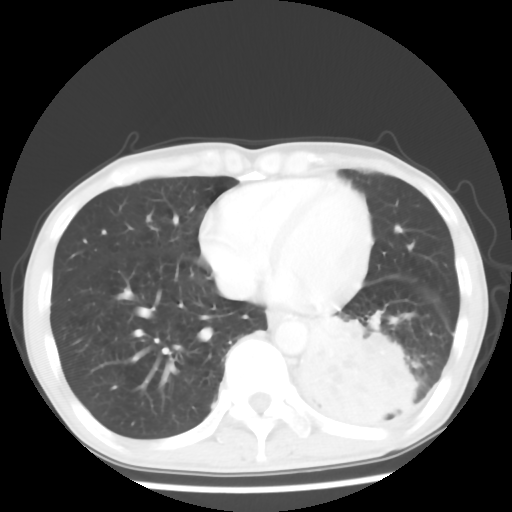
Chest CT, one axial slice; slice 20 of 64 in the series (ordered by position); reconstruction kernel STANDARD; lung window (W 1500 / L -600 HU); 5 mm slice thickness; 512 × 512 image matrix, field of view 313 × 313 mm. Male patient, age 68 years. From the clinical record (not read from this slice): clinical TNM (as recorded): T4 N0 M0.
Structures marked on this image (rectangle marked by the reading radiologist):
- lung tumour (recorded histology: squamous cell carcinoma): bounding box <306,312,401,415> (left, top, right, bottom; pixels)